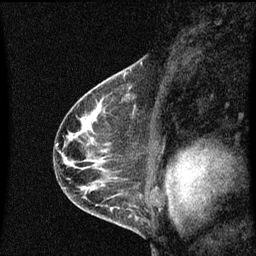
Breast MRI (dynamic contrast-enhanced), one sagittal slice; position 41 of 60 along the scan axis; dynamic contrast-enhanced series, image 2 of 3 at this slice position (ordered by acquisition); 1.5 T; TE 4.2 ms, TR 8.4 ms; 2 mm slice thickness; 256 × 256 image matrix, field of view 200 × 200 mm. Patient: female, 41 years.
Structures marked on this image (semi-automatically segmented with operator editing):
- analysis volume of interest (the breast-tissue region the enhancement analysis was run in; not a lesion): box from (x=121, y=74) to (x=142, y=99) px
- tumour enhancement mask (voxels above the 70 % enhancement threshold inside the analysis volume of interest): (x=124, y=74)–(x=126, y=77)